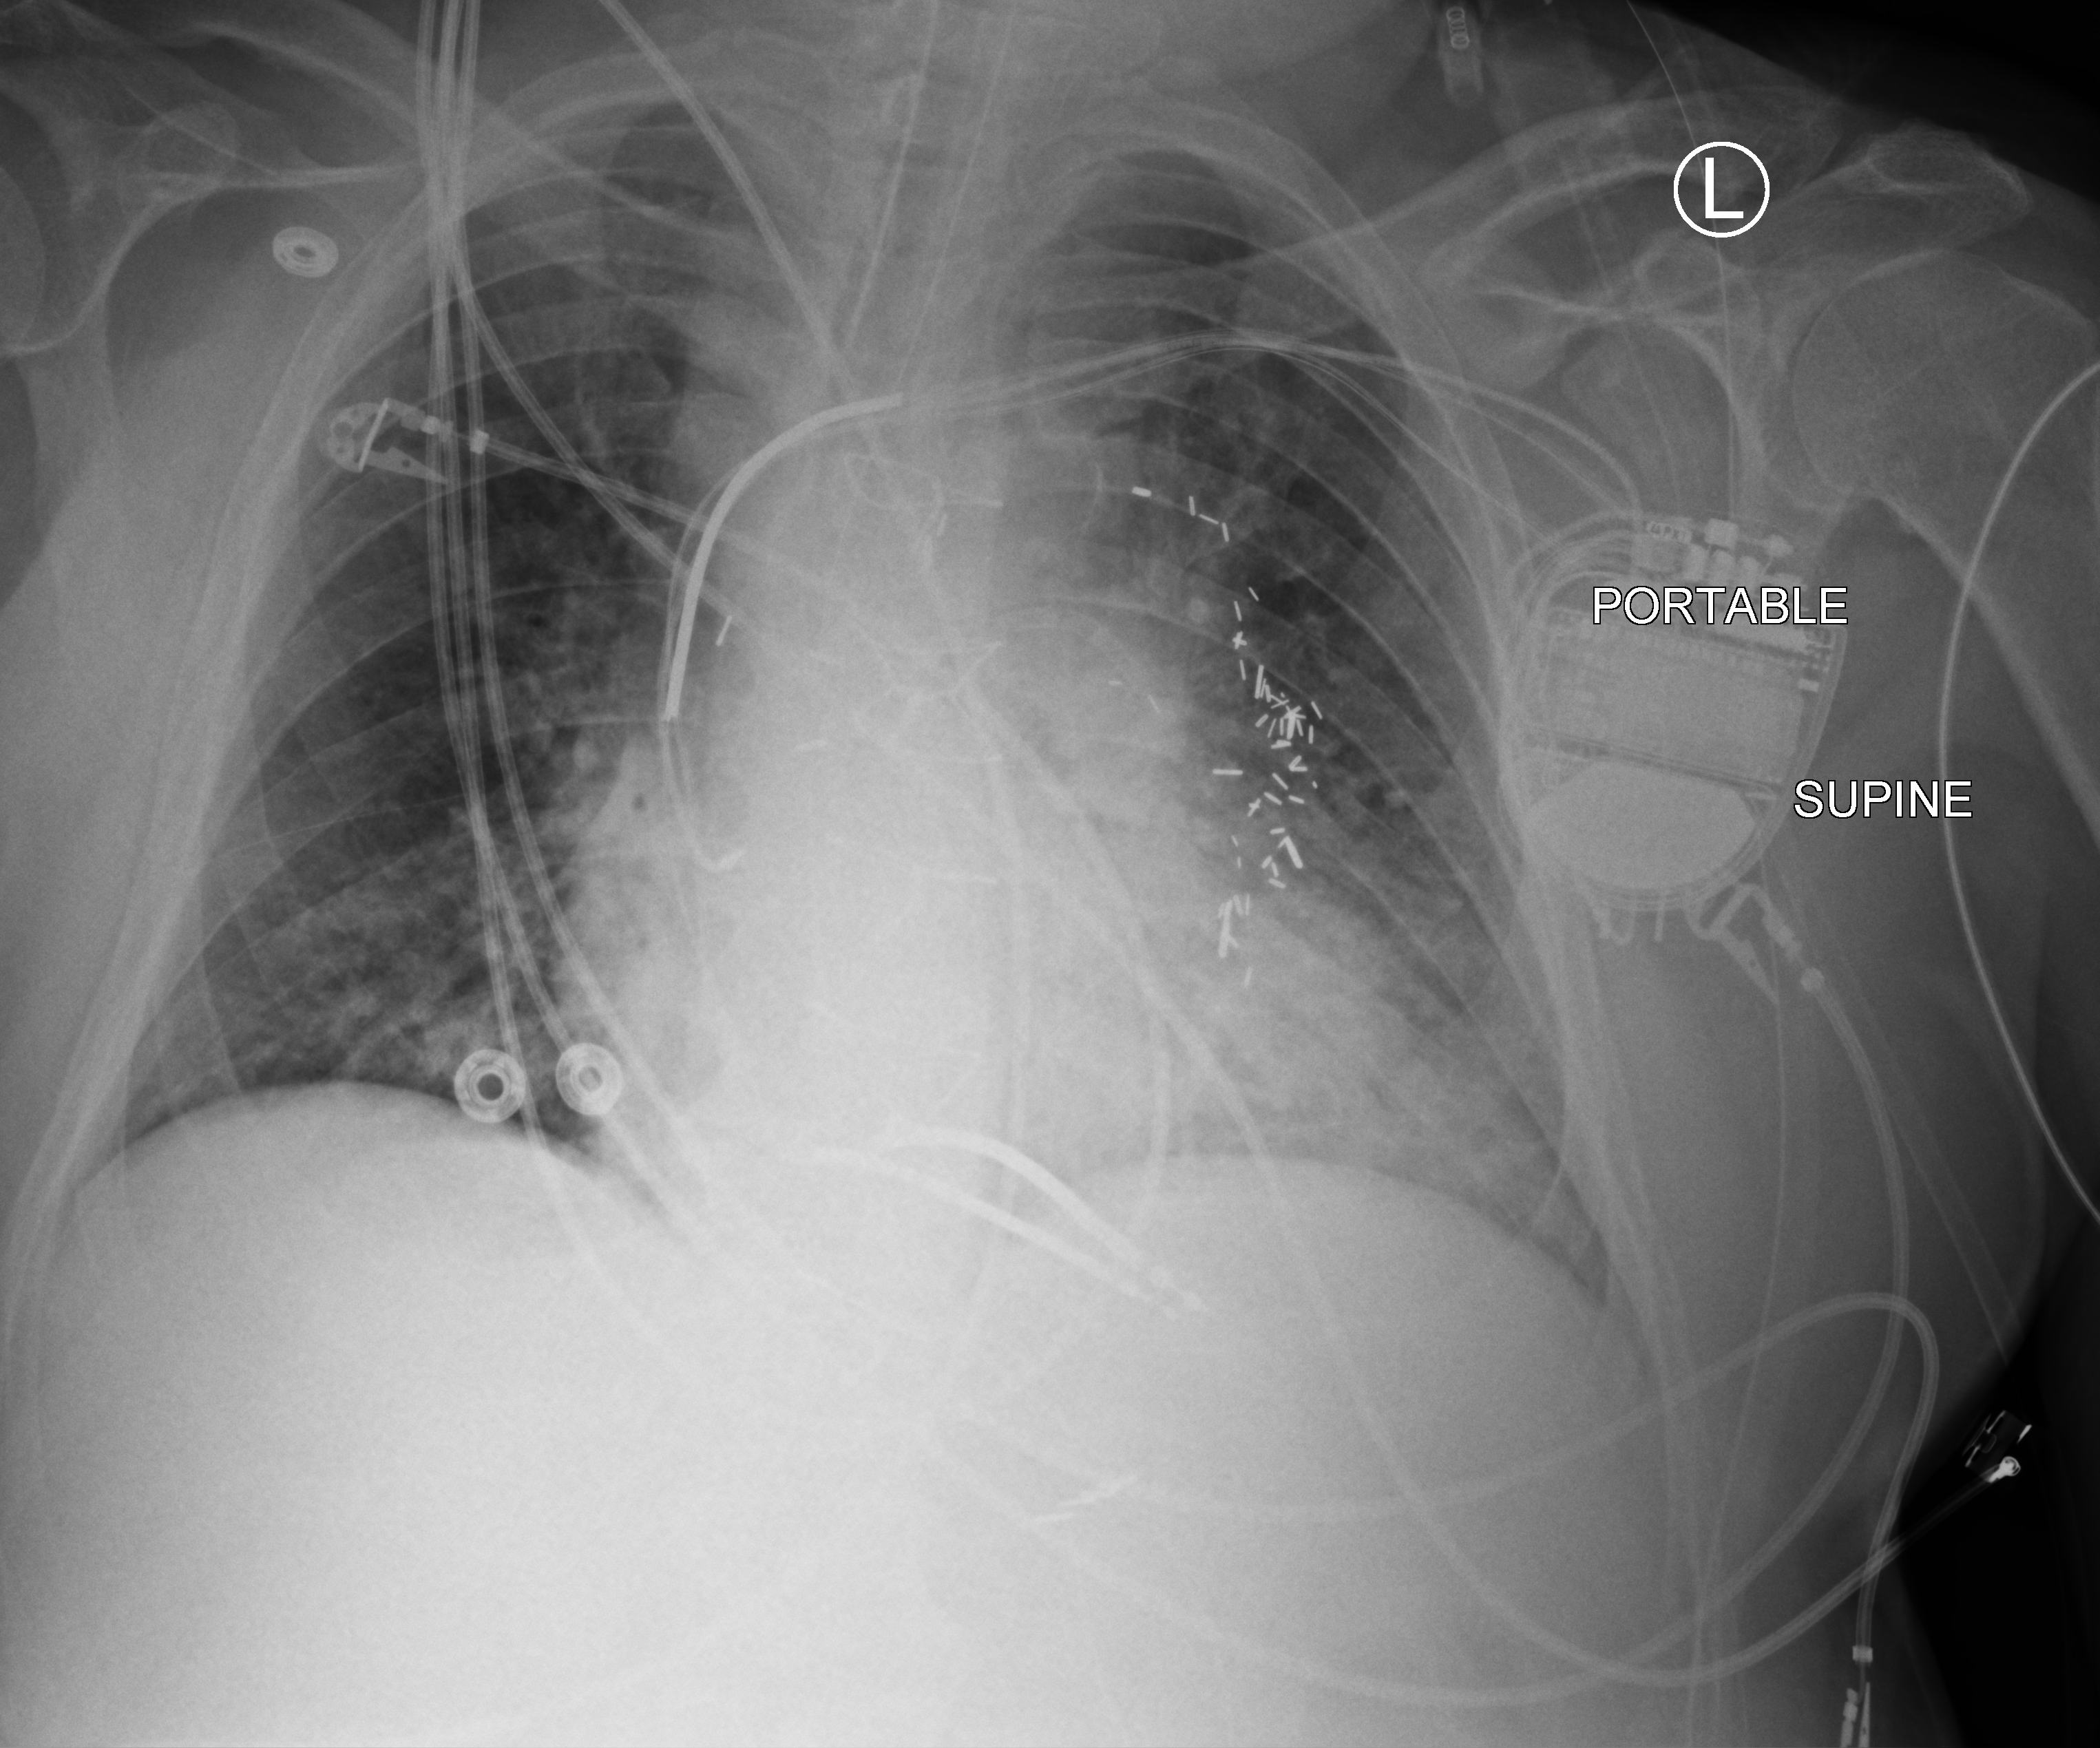
Bedside chest radiograph (computed radiography); anteroposterior (AP) projection. Male patient hospitalised with COVID-19, age 60–74 years.
Hospital-stay facts (about this admission, not read from this image; timing relative to this image not recorded):
- mechanically ventilated during this hospital stay: yes
- length of hospital stay: 55 days
- admitted to intensive care during this hospital stay: yes